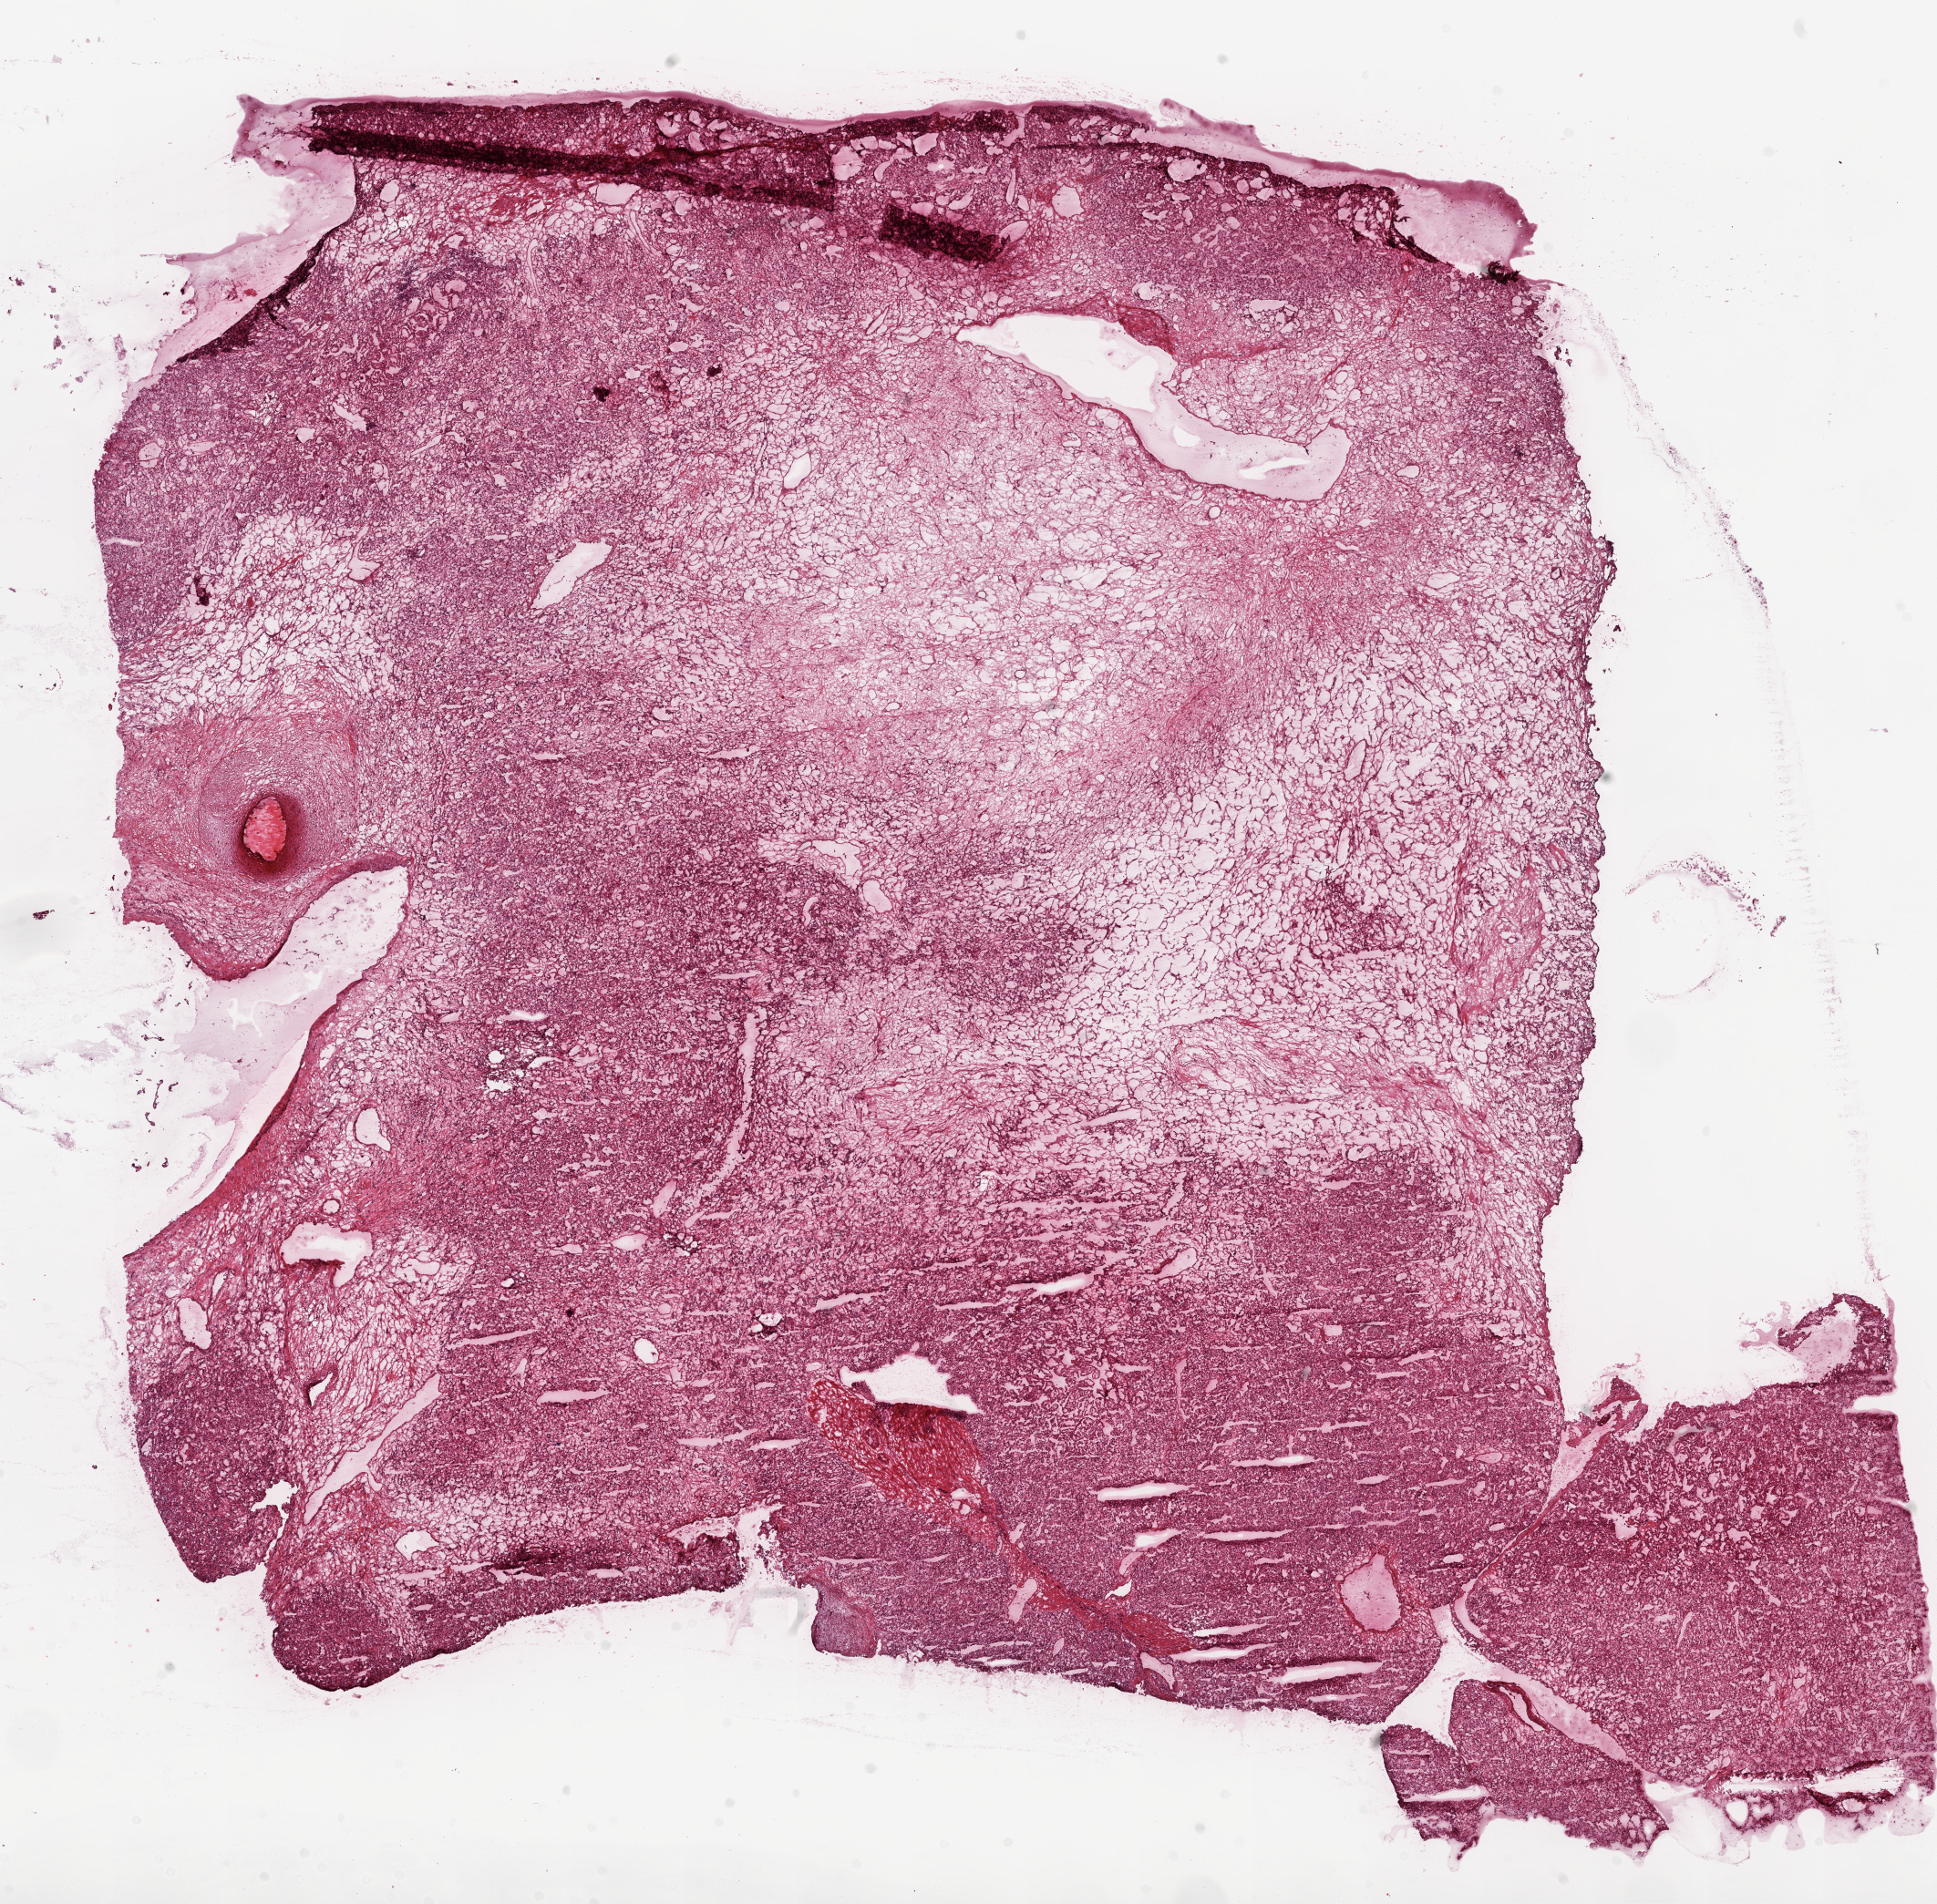
Whole-slide histology image, Hematoxylin and eosin (H&E) stained, low-resolution overview of the scanned area, about 17.1 x 16.8 mm (slide scanned at 20x), frozen section from the top of the tissue portion, primary tumour sample from the kidney. Female, age 46 years at initial diagnosis.
Diagnosis: Clear cell adenocarcinoma, NOS.